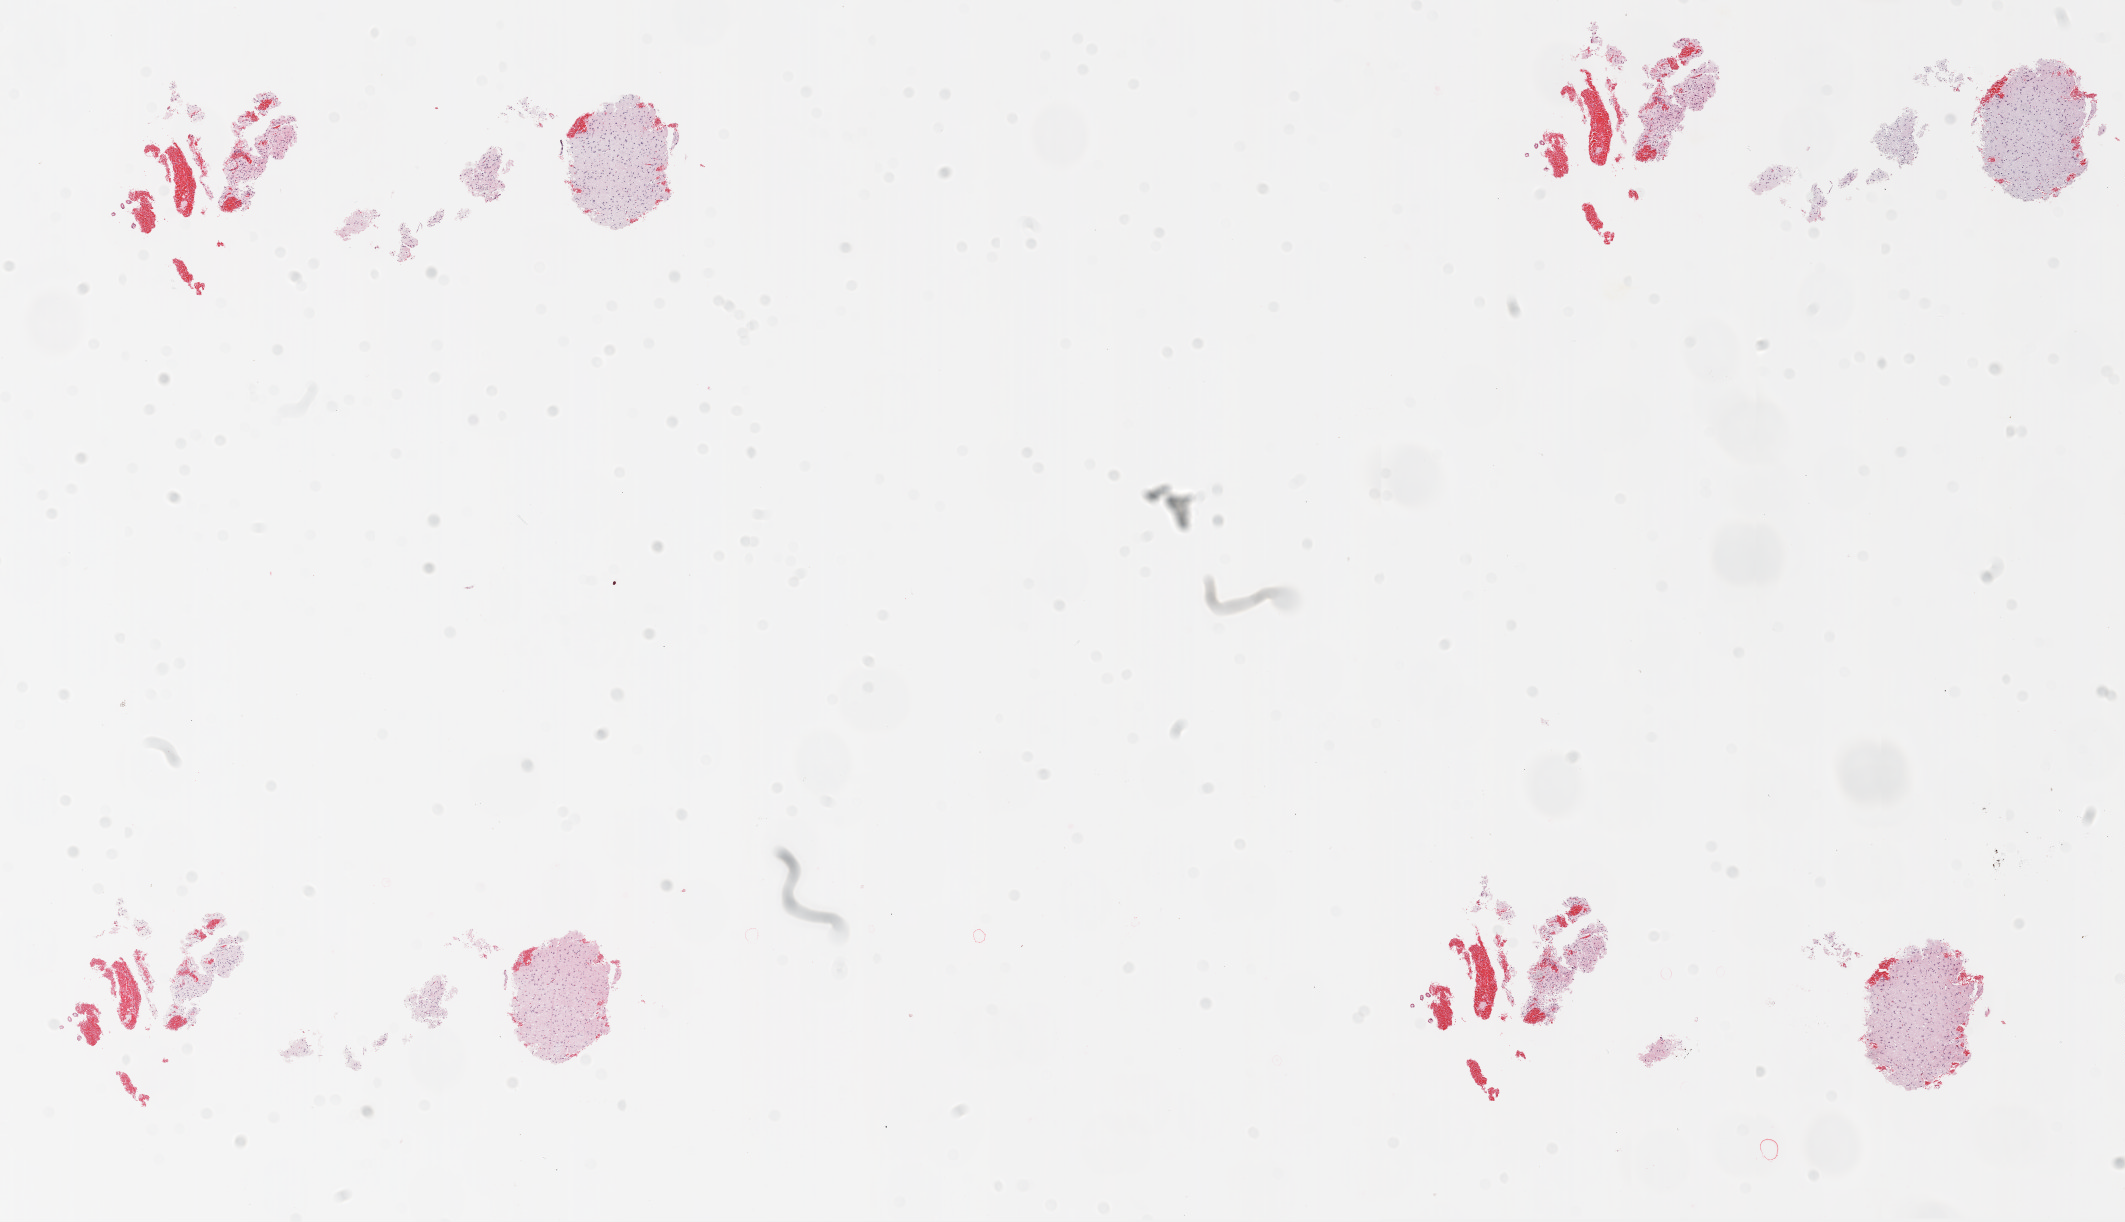
Whole-slide histology image, H&E-stained — low-resolution overview of the scanned area, about 17.1 x 9.8 mm (slide scanned at 20x). FFPE section. Brain, primary tumour sample. Male patient; age at initial diagnosis 61 years.
• histologic diagnosis: Glioblastoma